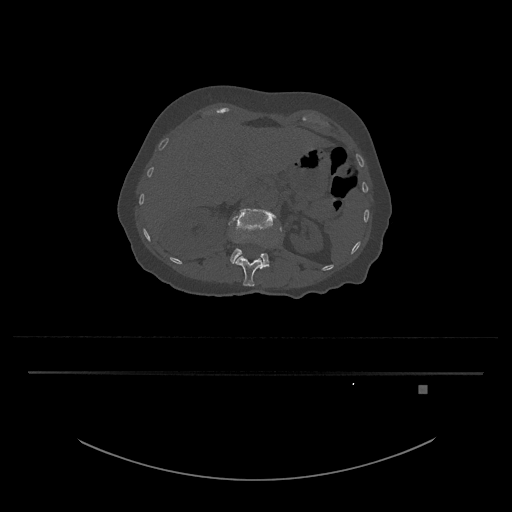
CT including the spine, one axial slice; slice 528 of 797 in the series (ordered by position); reconstruction kernel Br40s/3; bone window (W 1800 / L 400 HU); 0.5 mm slice thickness; 512 × 512 image matrix, field of view 500 × 500 mm. Patient: female, 57 years. From the clinical record (not read from this slice): primary cancer: cervical.
Annotated regions visible in this slice (semi-automatically segmented with operator editing):
- L1 vertebra: bounding box <234,227,283,287> (left, top, right, bottom; pixels)